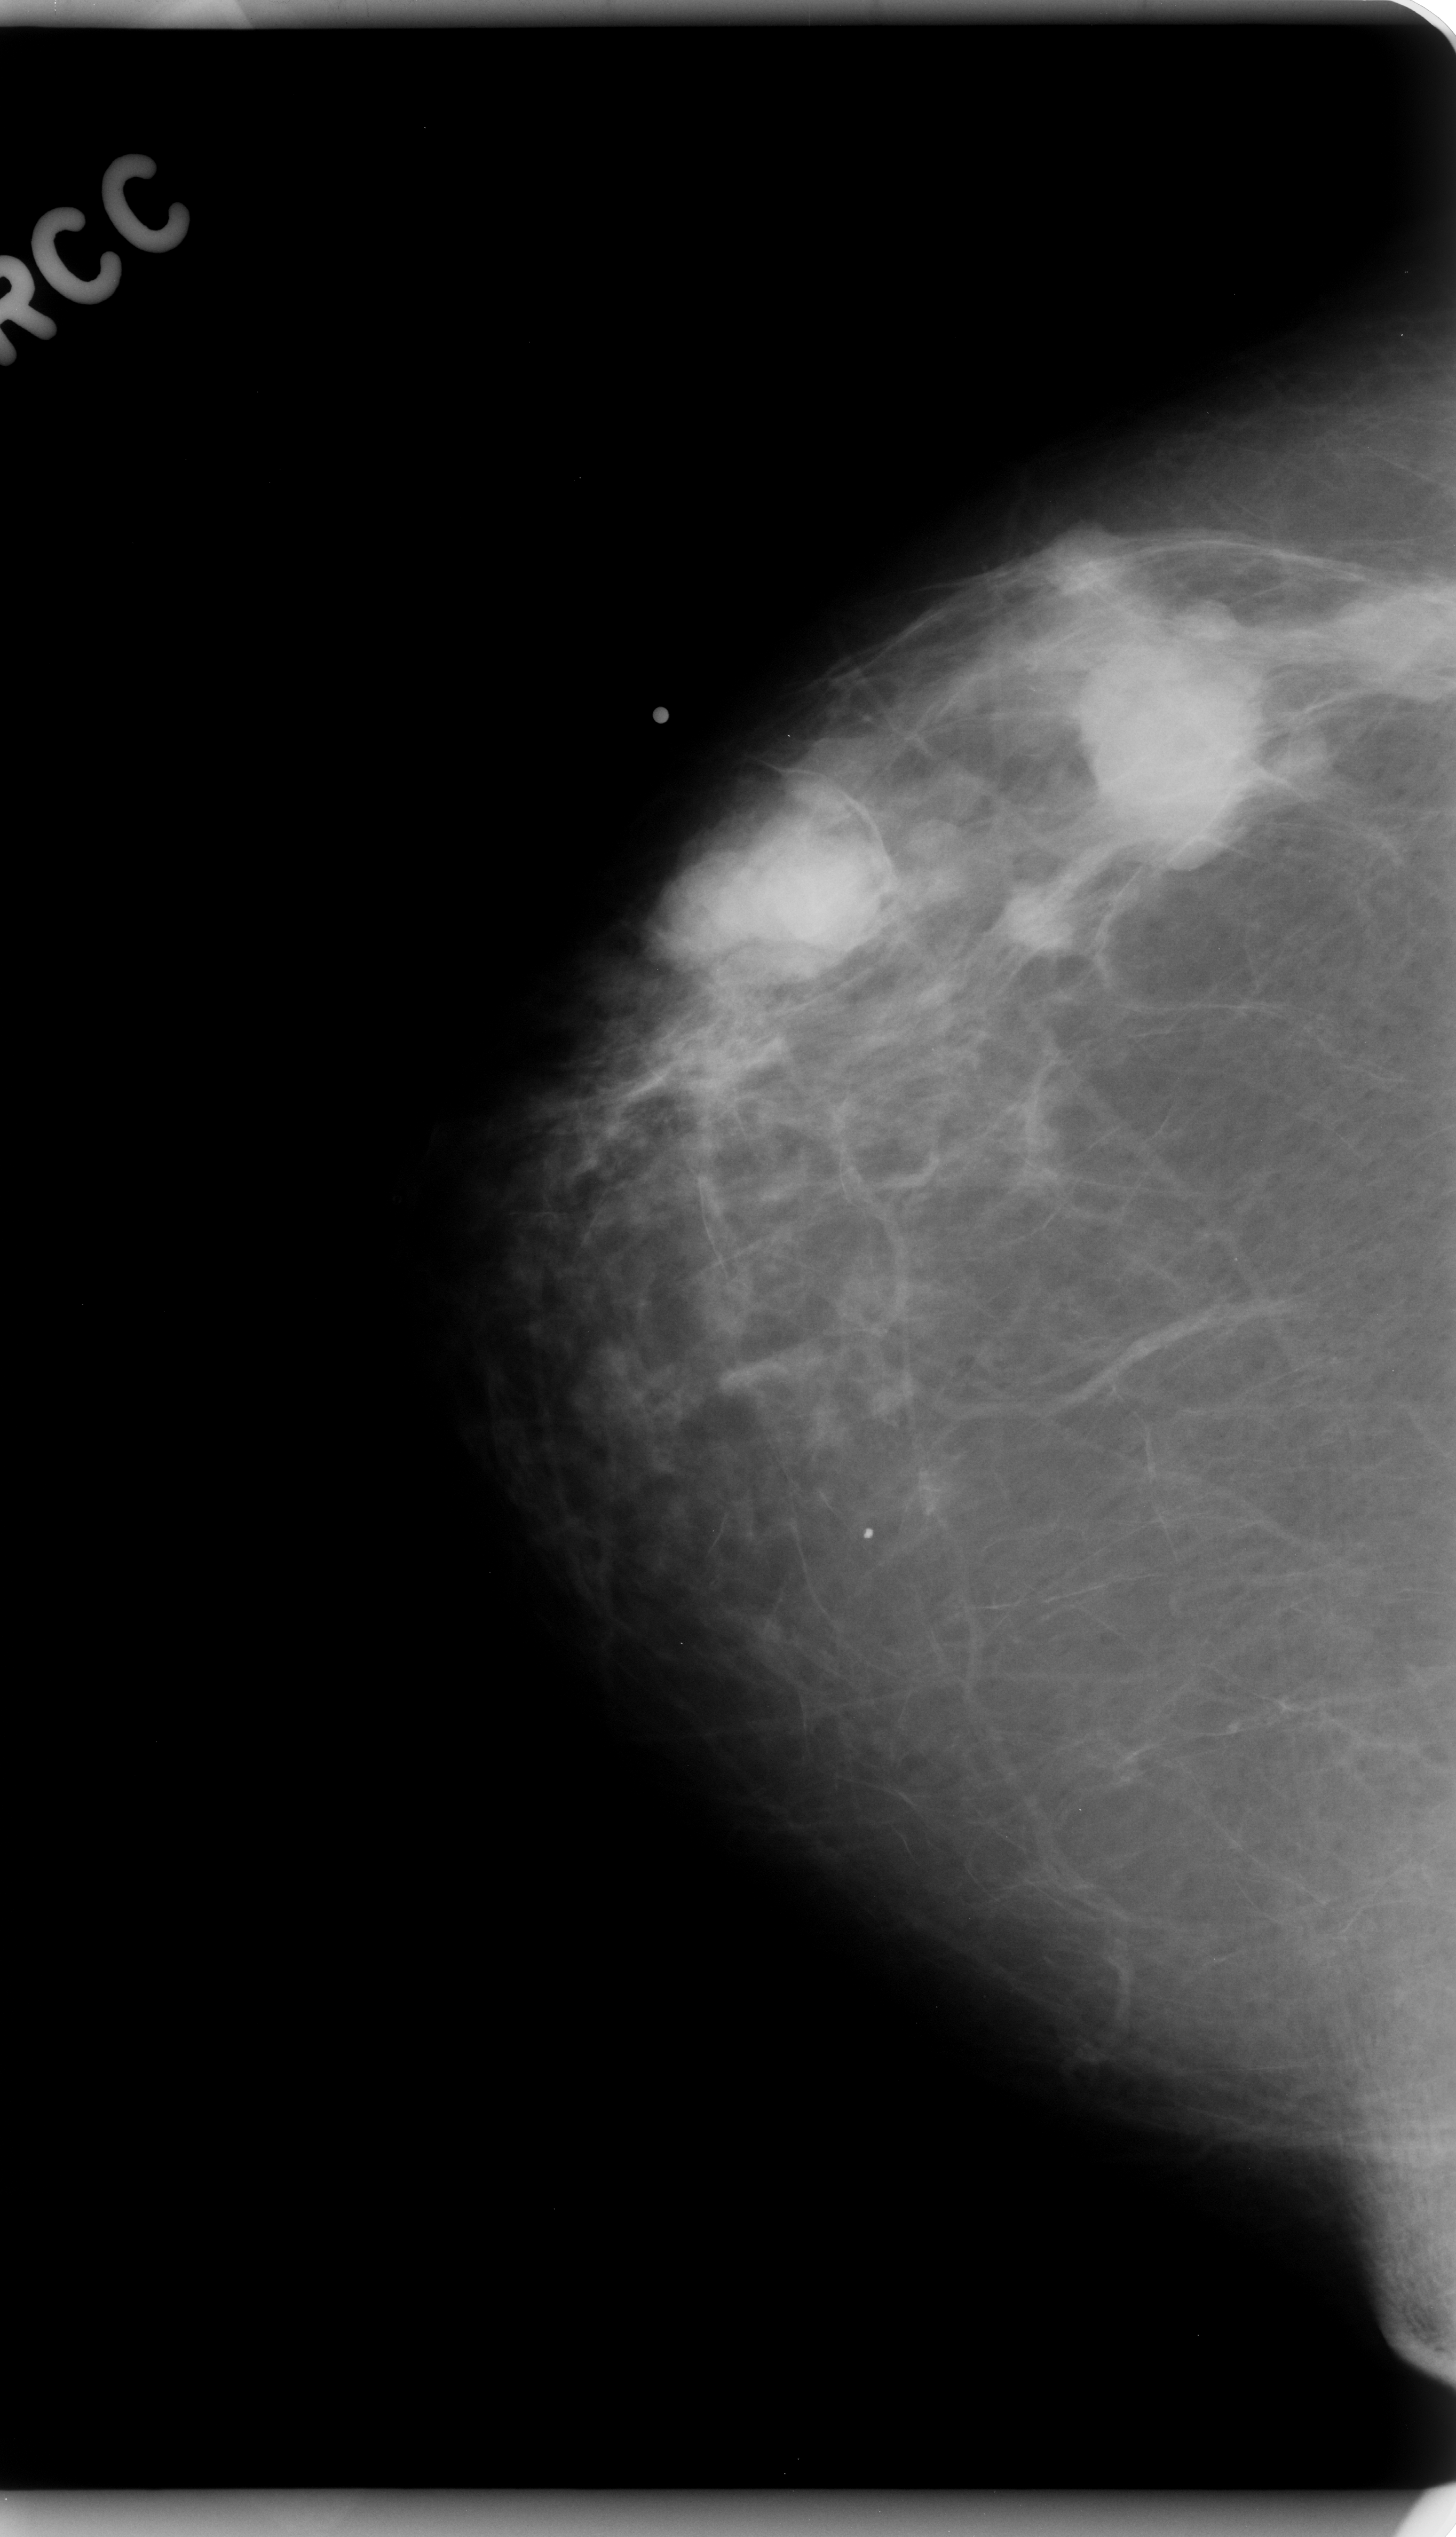
Scanned film-screen mammogram. Right breast. Craniocaudal (CC) view. BI-RADS breast density category 1 (scale 1–4). 1456 × 2537 image matrix.
Marked abnormalities (boxes around the expert regions of interest):
- mass, shape lobulated, margins circumscribed; BI-RADS assessment category 5; subtlety rating 5 on a 1 (subtle) to 5 (obvious) scale; pathology (as recorded): malignant: bounding box <642,752,967,1018> (left, top, right, bottom; pixels)